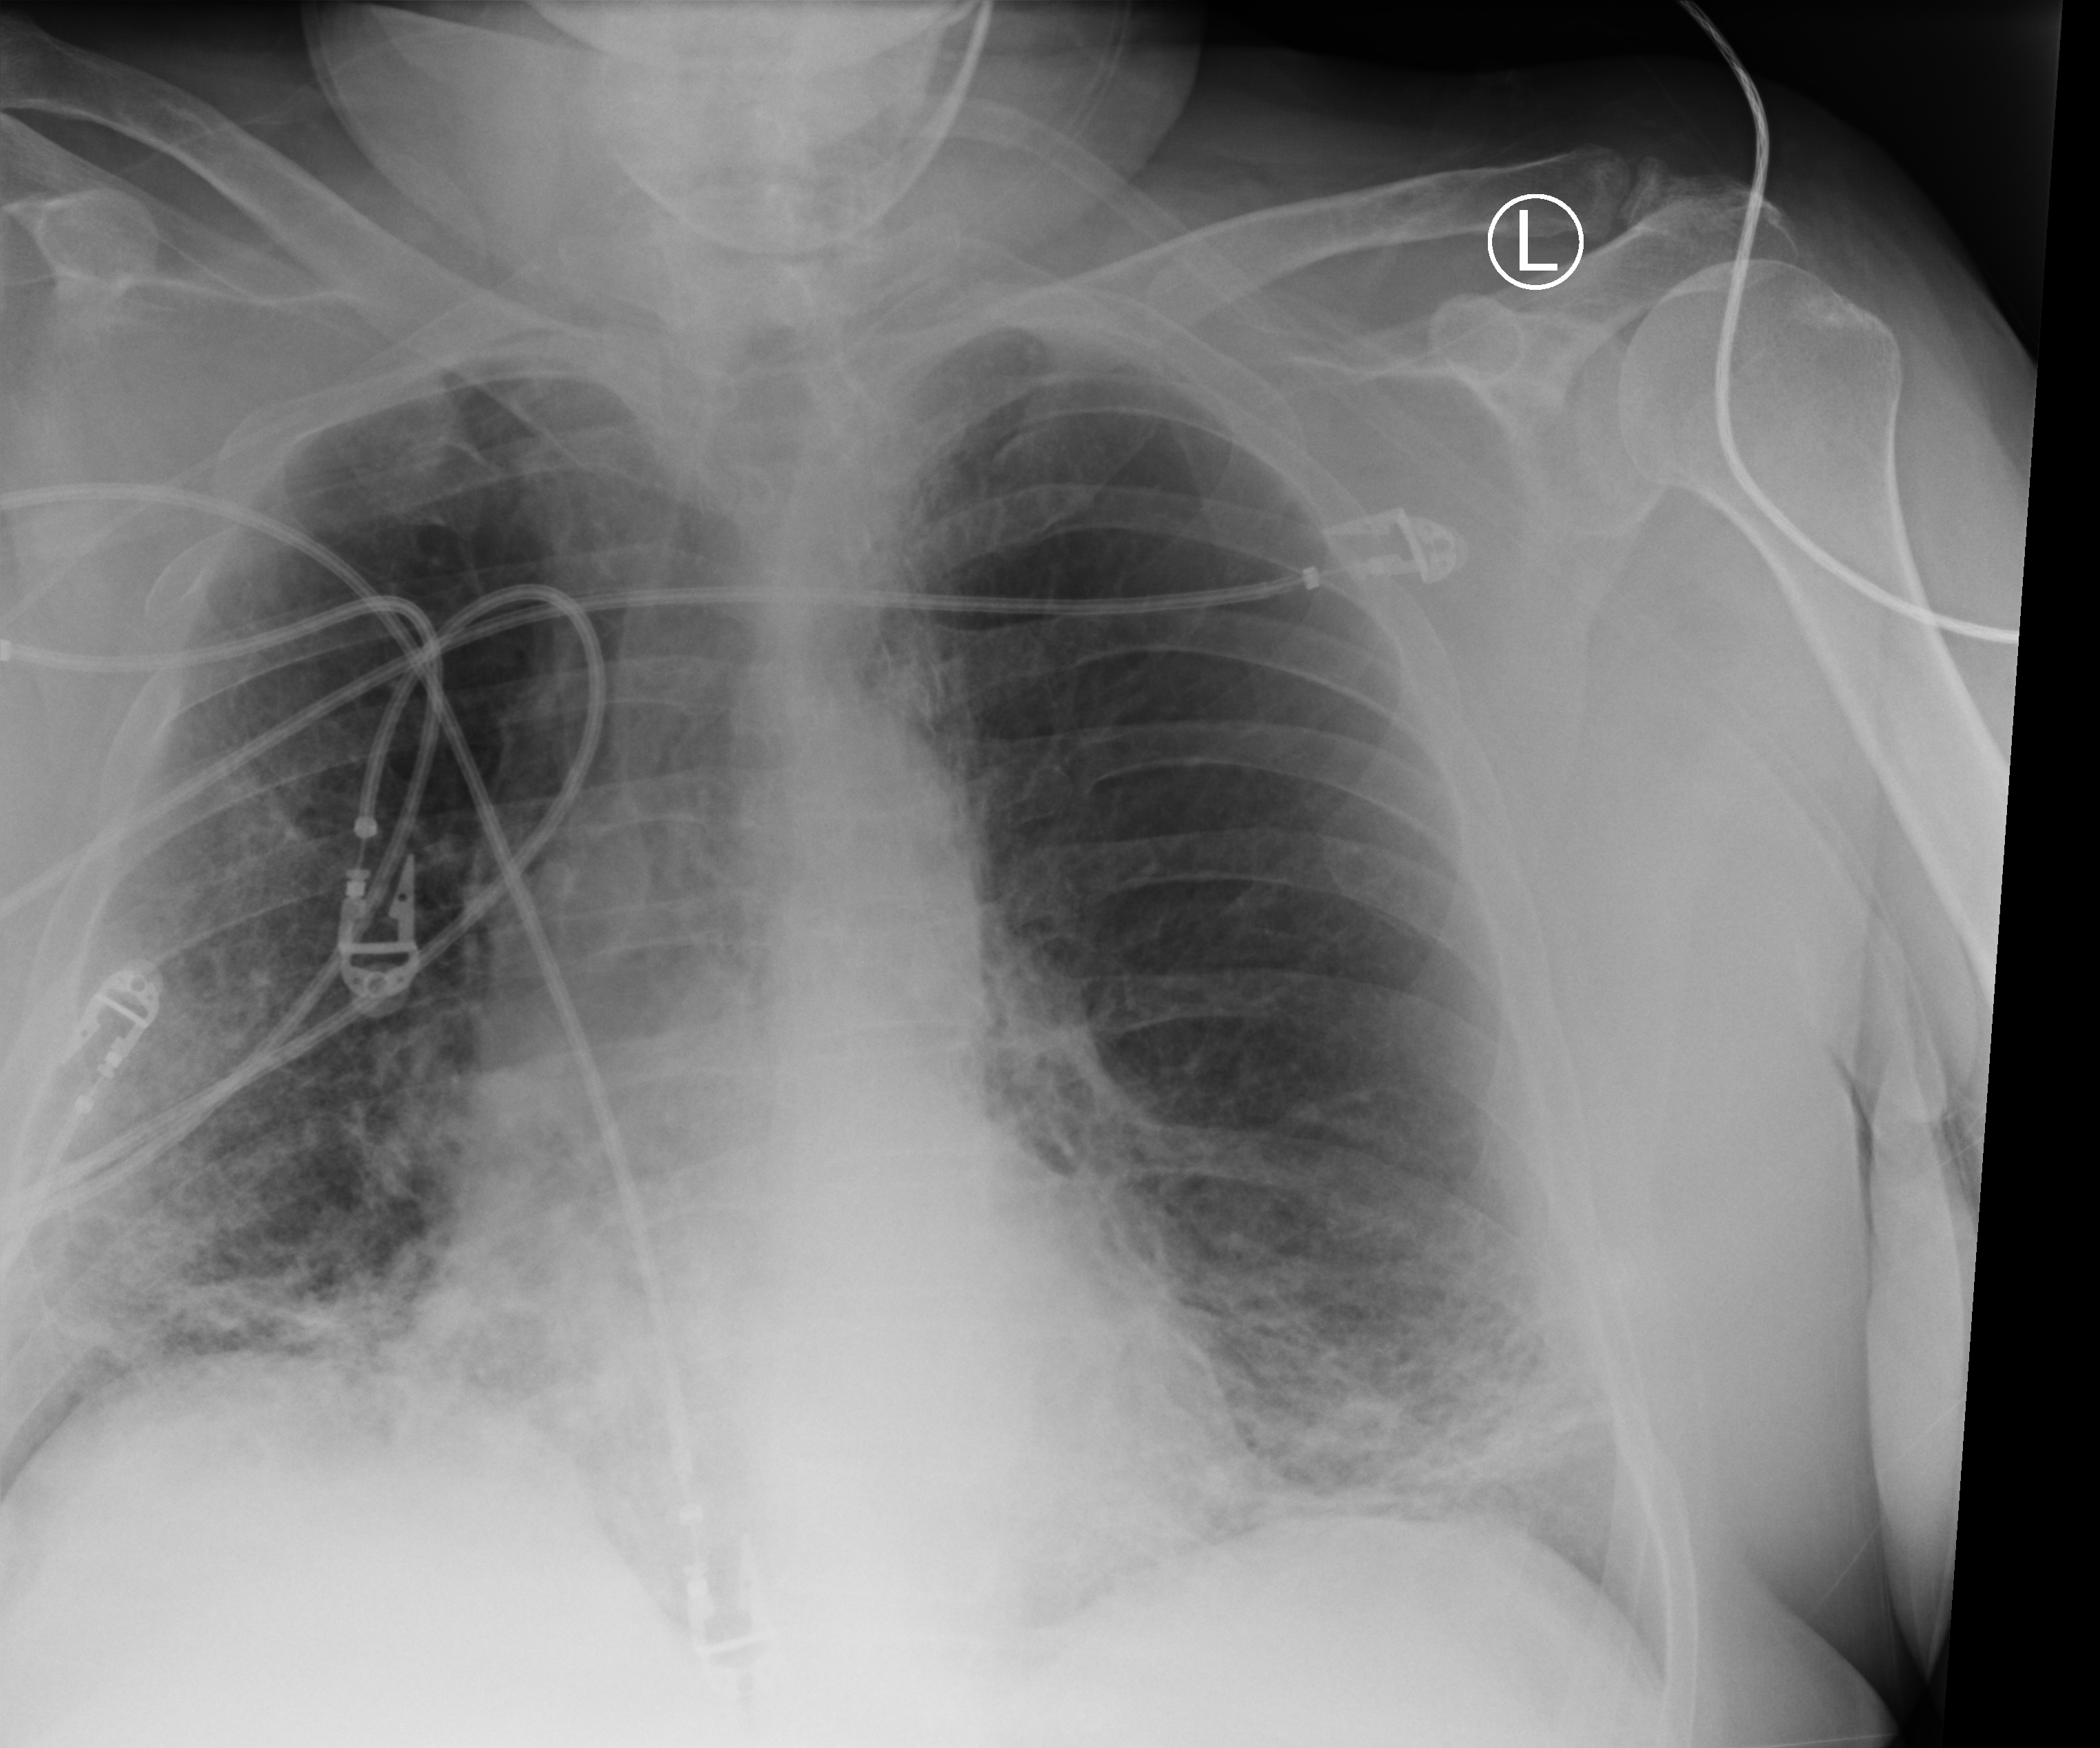
Bedside chest radiograph (computed radiography). Patient hospitalised with COVID-19; male, aged 60–74 years.
Hospital-stay facts (about this admission, not read from this image; timing relative to this image not recorded): COPD (admission record): no; admitted to intensive care during this hospital stay: no; smoking status (admission record): former.